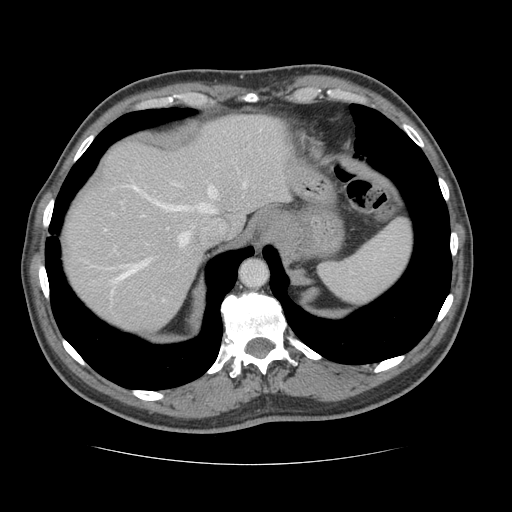
Contrast-enhanced abdominal CT, one axial slice; position 107 of 134 along the scan axis; reconstruction kernel STANDARD; 120 kVp; intravenous contrast given; soft-tissue window (W 400 / L 40 HU); 2.5 mm slice thickness; 512 × 512 image matrix, field of view 377 × 377 mm. Male patient, age 68 years. Case-level facts recorded for this patient, not image findings: diagnosis: colorectal cancer liver metastases, imaged before liver resection; multiple liver metastases: yes; largest metastasis: 2.2 cm; disease in both lobes: no.
Annotated regions visible in this slice (manually delineated by an expert):
- hepatic veins: bounding box [x1, y1, x2, y2] px = [105, 181, 246, 281]
- liver: [63, 115, 288, 332]
- planned liver remnant (the part of the liver to remain after resection): [63, 115, 288, 315]